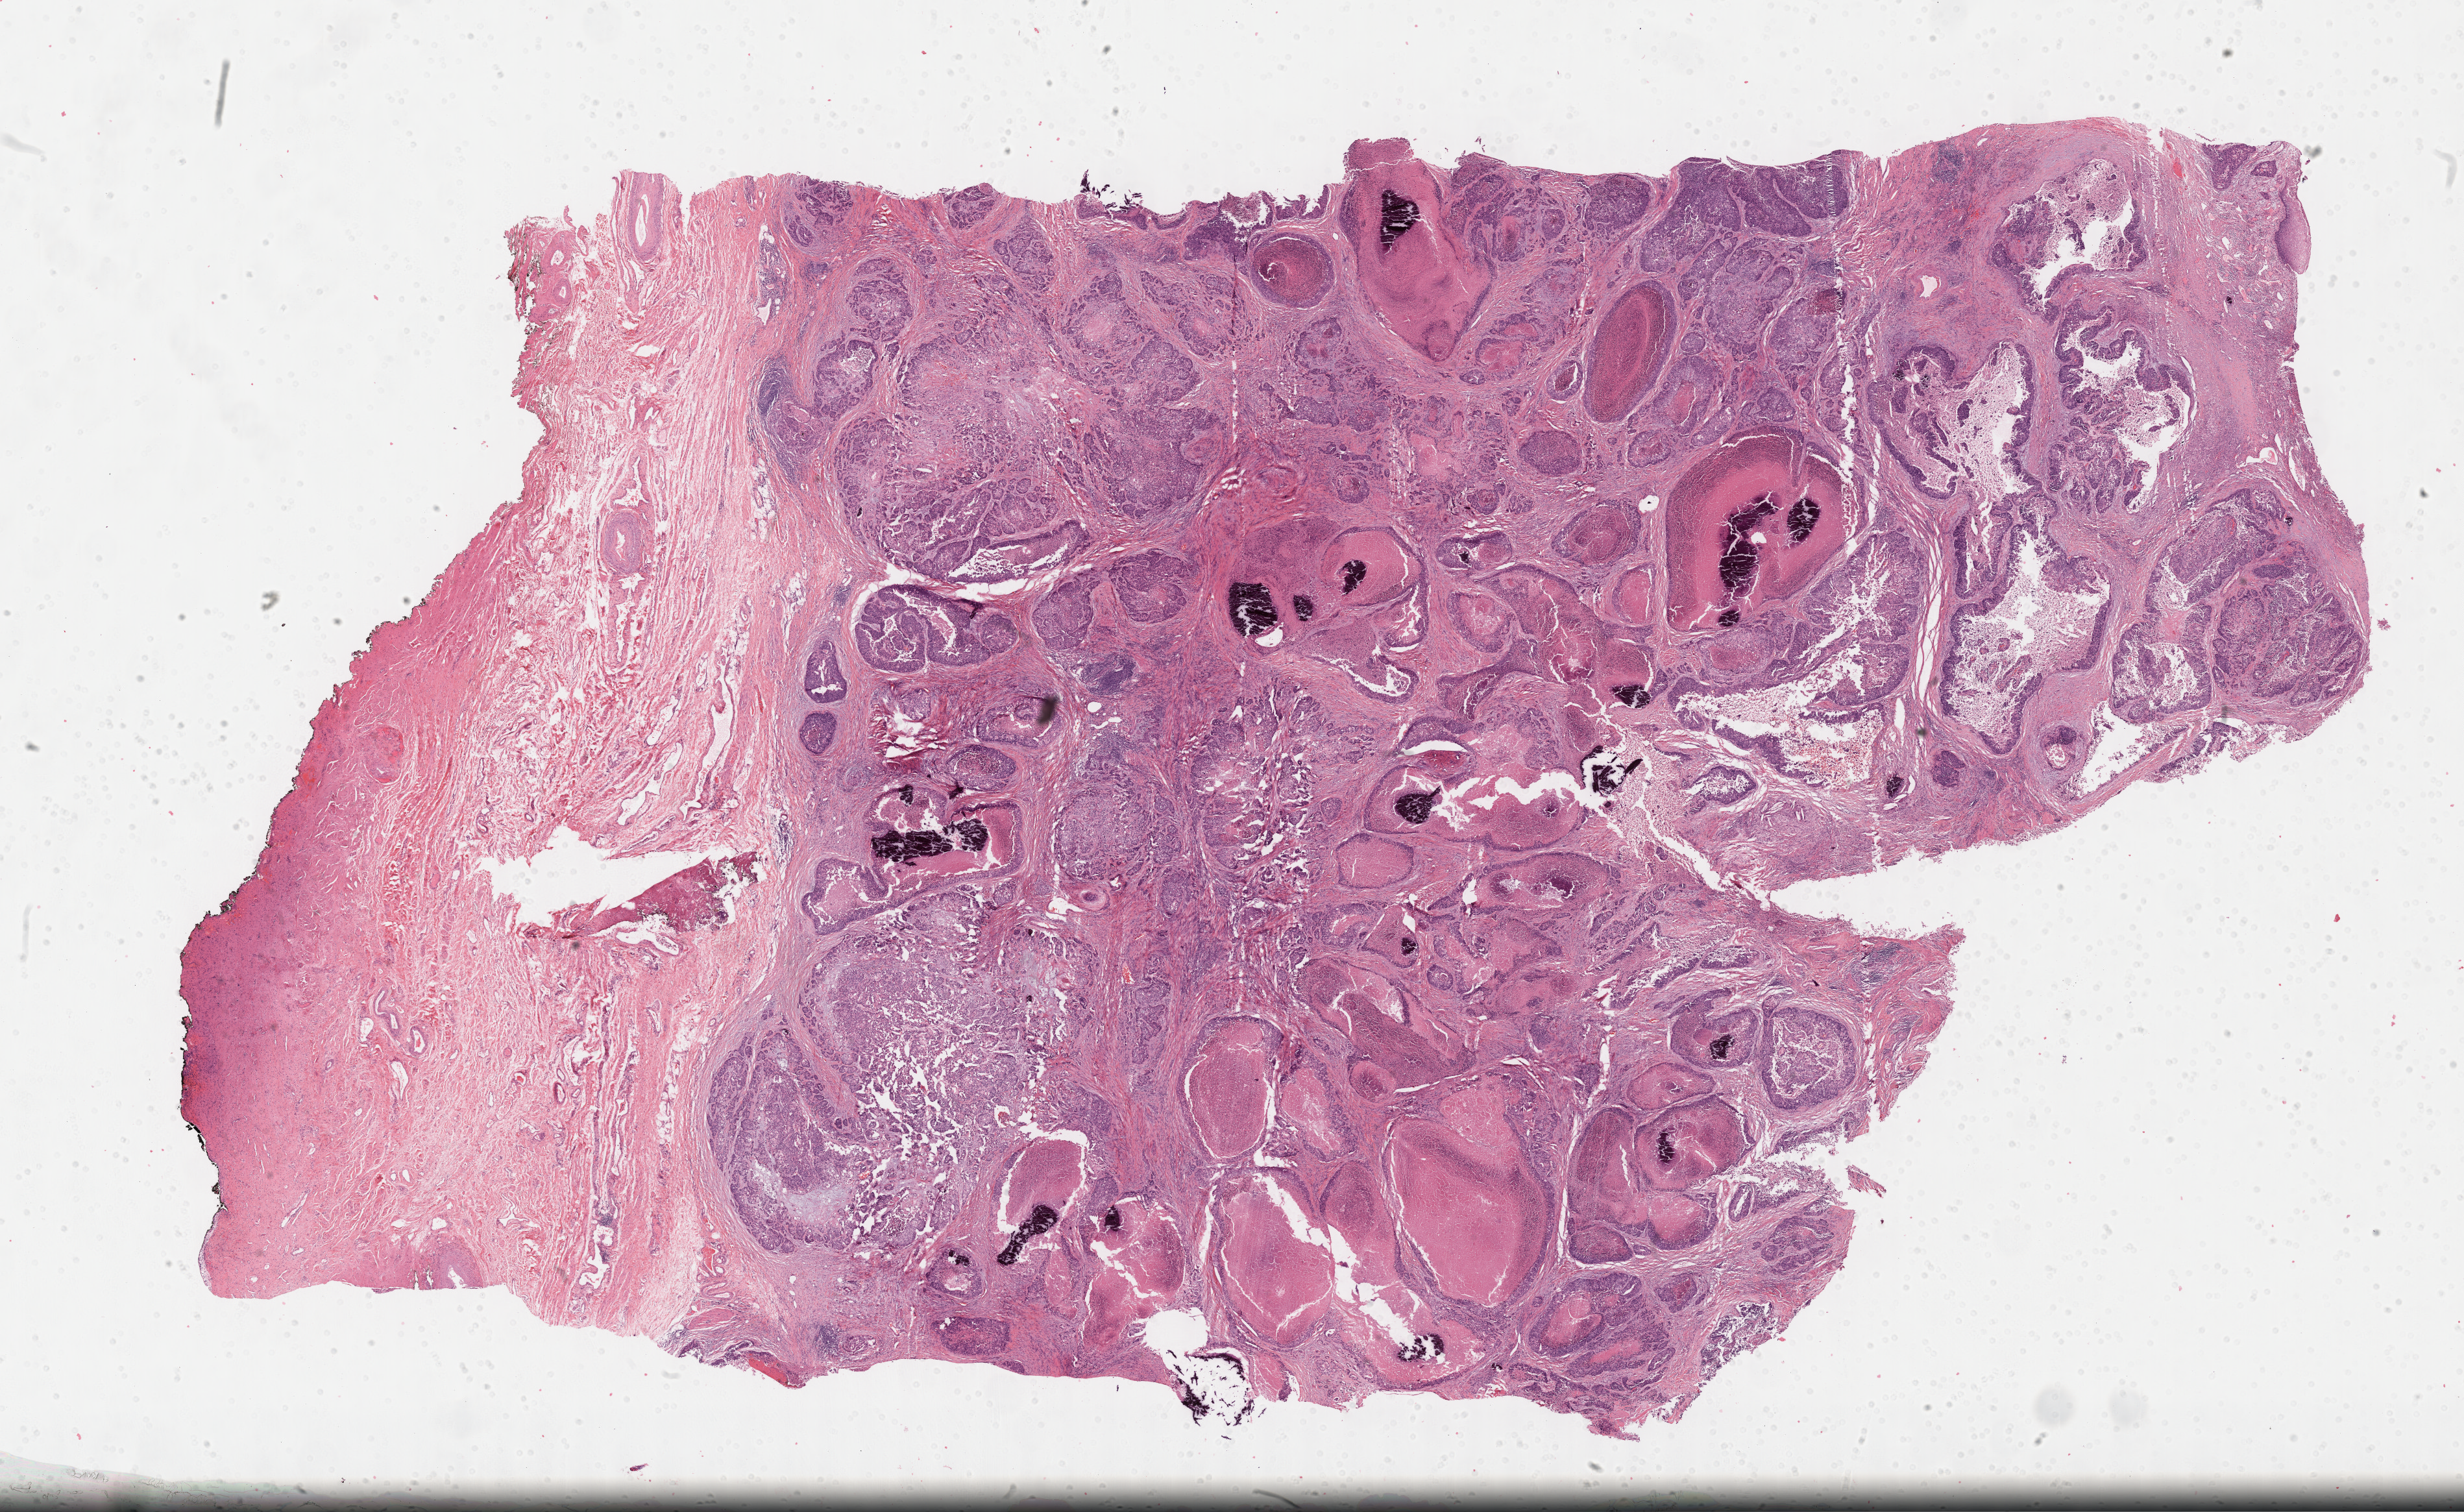
Digitized H&E-stained tissue section (whole slide) — shown as a low-resolution overview of the whole scanned area (about 30.7 x 18.8 mm, slide scanned at 40x); formalin-fixed paraffin-embedded (FFPE) diagnostic section; sample: primary tumour, bladder. Patient: female, age at initial diagnosis 74 years. Histologic grade: high grade.
Histologic diagnosis: Transitional cell carcinoma. AJCC pathologic stage: II (6th edition).